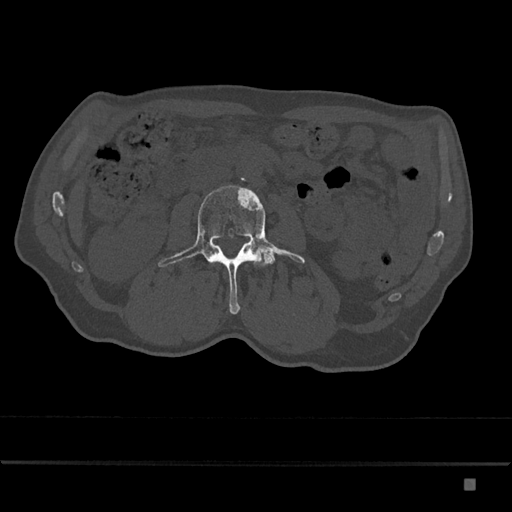
CT including the spine, one axial slice; position 410 of 797 along the scan axis; 120 kVp; bone window (W 1800 / L 400 HU); 512 × 512 image matrix, field of view 390 × 390 mm. Male patient, age 72 years. Case-level facts recorded for this patient, not image findings: primary cancer: prostate.
Outlined on this slice (semi-automatic segmentation, software-assisted and operator-edited):
- L3 vertebra: bounding box <158,185,305,314> (left, top, right, bottom; pixels)
- L4 vertebra: <266,259,270,265>